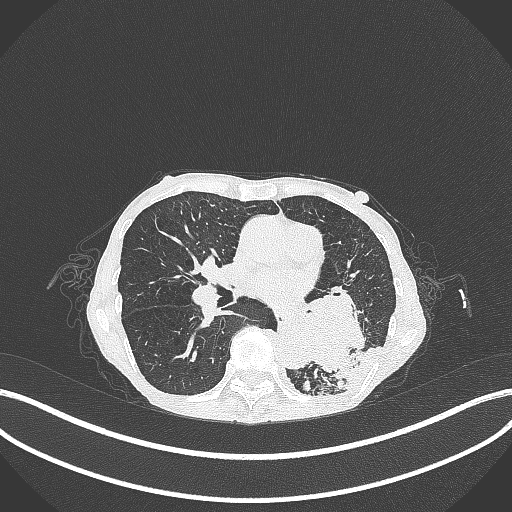
Chest CT, one axial slice. Reconstruction kernel B70f. Lung window (W 1500 / L -600 HU). 1 mm slice thickness. 512 × 512 image matrix. Female patient, age 70 years. Case-level facts recorded for this patient, not image findings: clinical TNM (as recorded): T3 N0 M0.
Outlined on this slice (rectangle marked by the reading radiologist):
- lung tumour (recorded histology: small cell carcinoma): box from (x=291, y=281) to (x=372, y=382) px